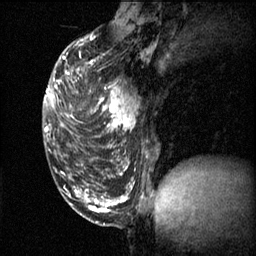
Breast MRI (dynamic contrast-enhanced), one sagittal slice; slice 23 of 60 in the series (ordered by position); 3 images stored at this slice position (order not interpretable as contrast timing); 1.5 T; TE 4.2 ms, TR 11.1 ms; 2 mm slice thickness; 256 × 256 image matrix, field of view 180 × 180 mm. Female patient, age 50 years.
Outlined on this slice (semi-automatically segmented with operator editing):
- analysis volume of interest (the breast-tissue region the enhancement analysis was run in; not a lesion): box from (x=69, y=68) to (x=139, y=141) px
- tumour enhancement mask (voxels above the 70 % enhancement threshold inside the analysis volume of interest): (x=69, y=68)–(x=136, y=137)